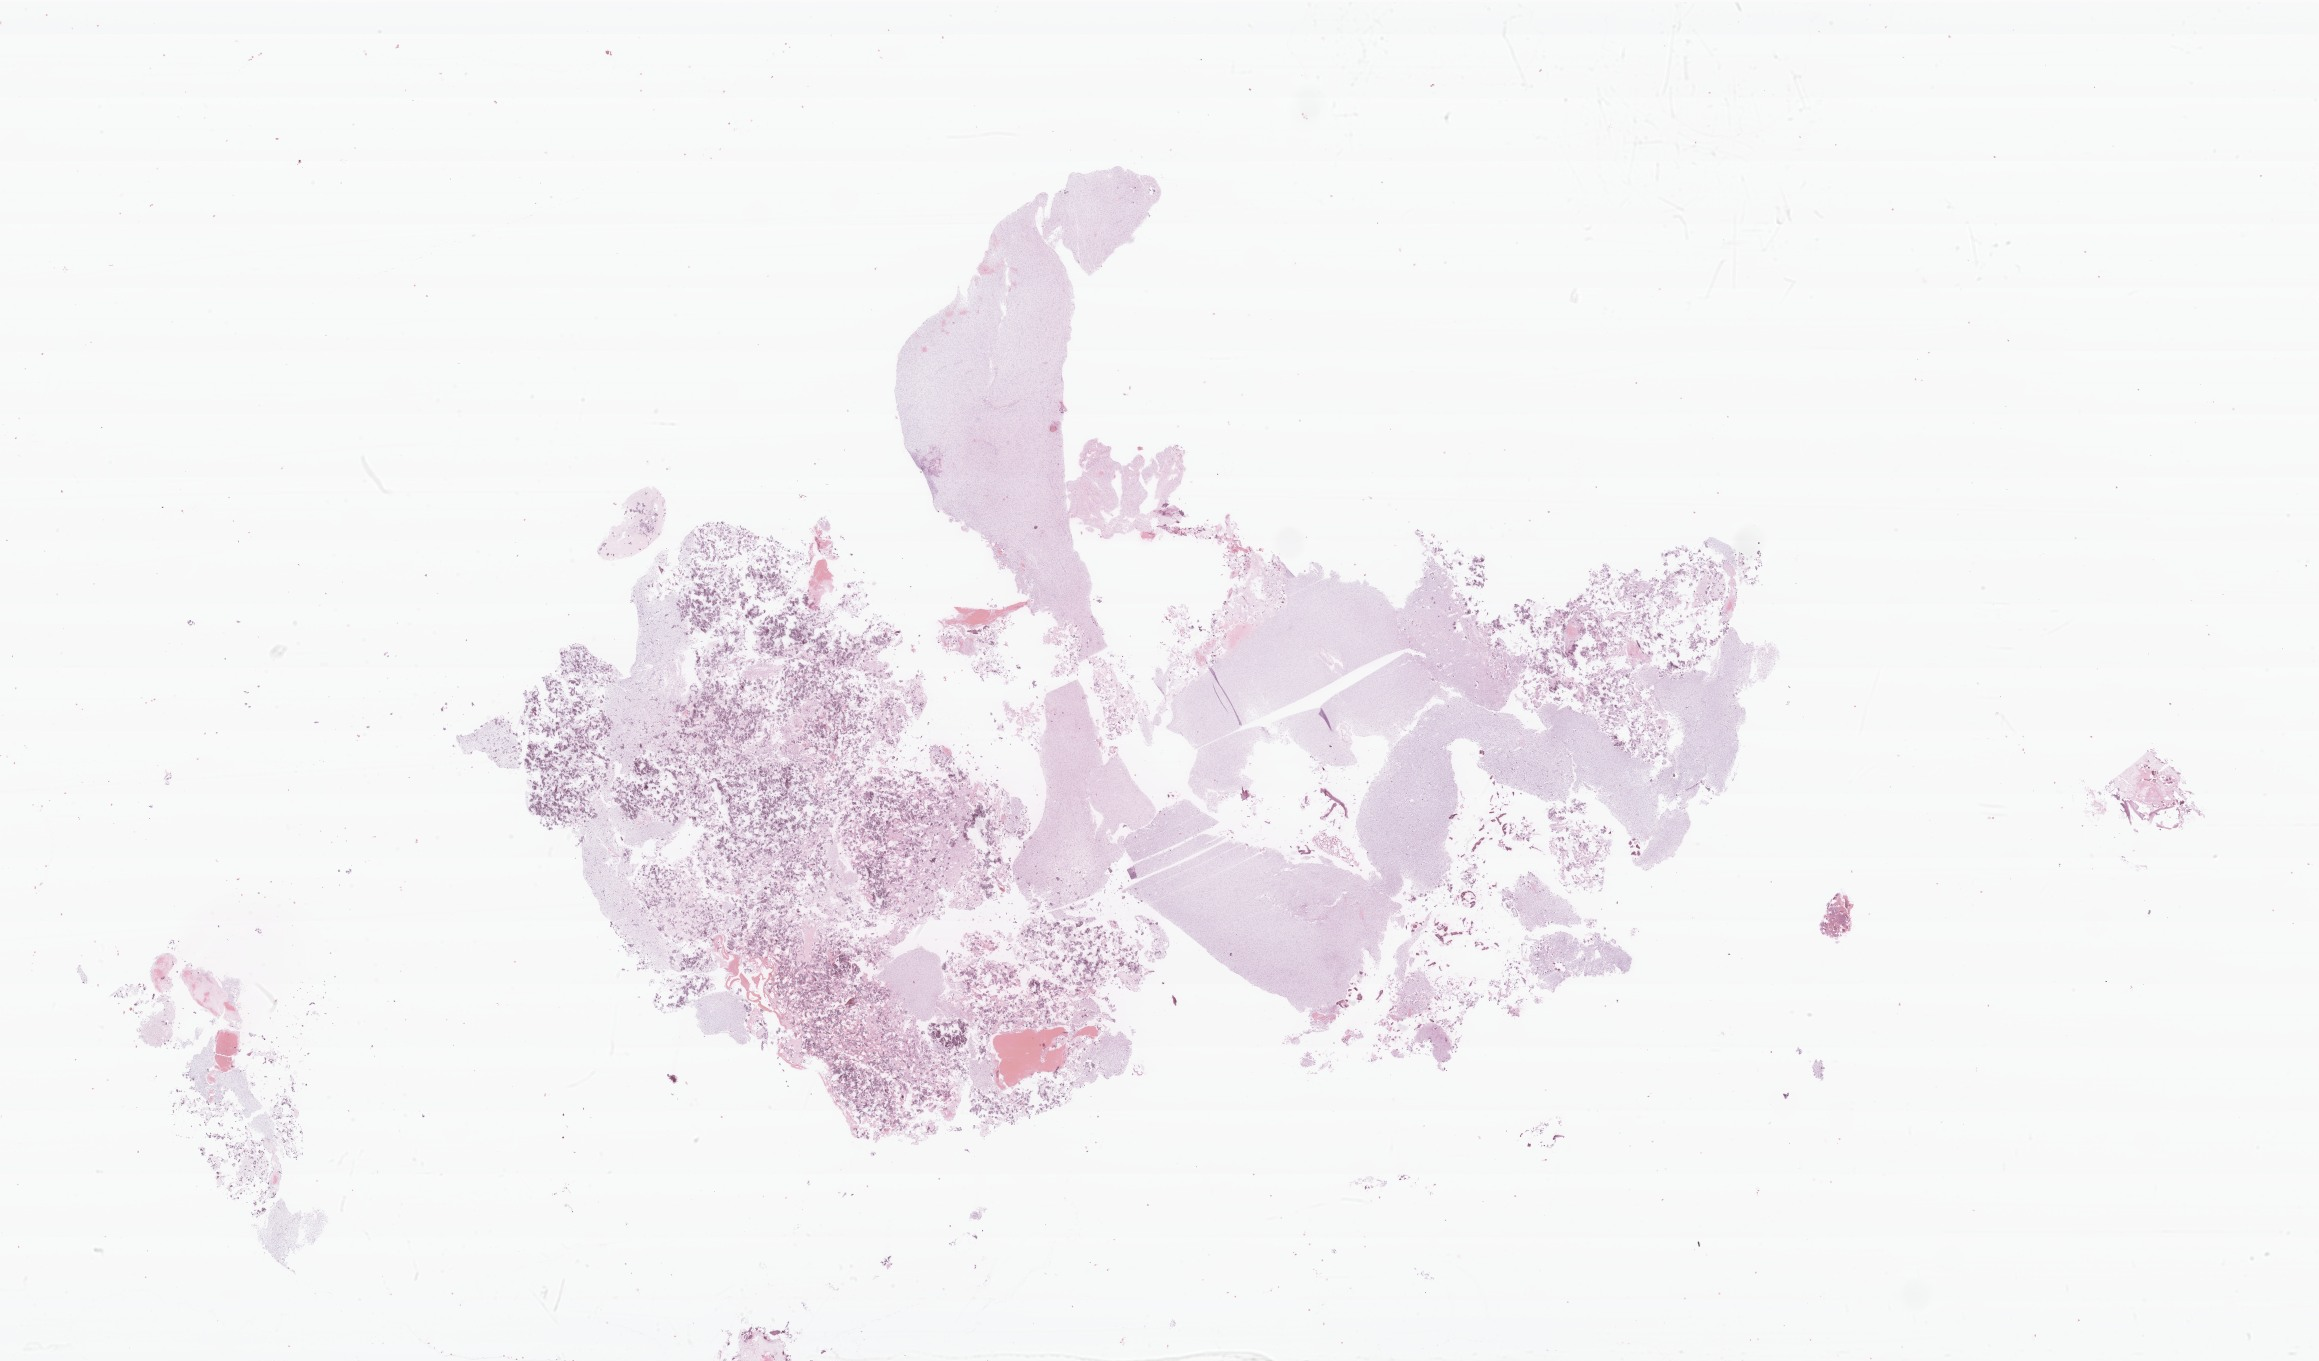
Haematoxylin and eosin whole-slide image of tumor tissue from the cerebrum — a low-resolution overview of the entire scanned area, about 39.0 x 22.9 mm, formalin-fixed, paraffin-embedded (FFPE) tissue. Female patient, age 120 months (10 years).
- diagnosis: Glioma, malignant